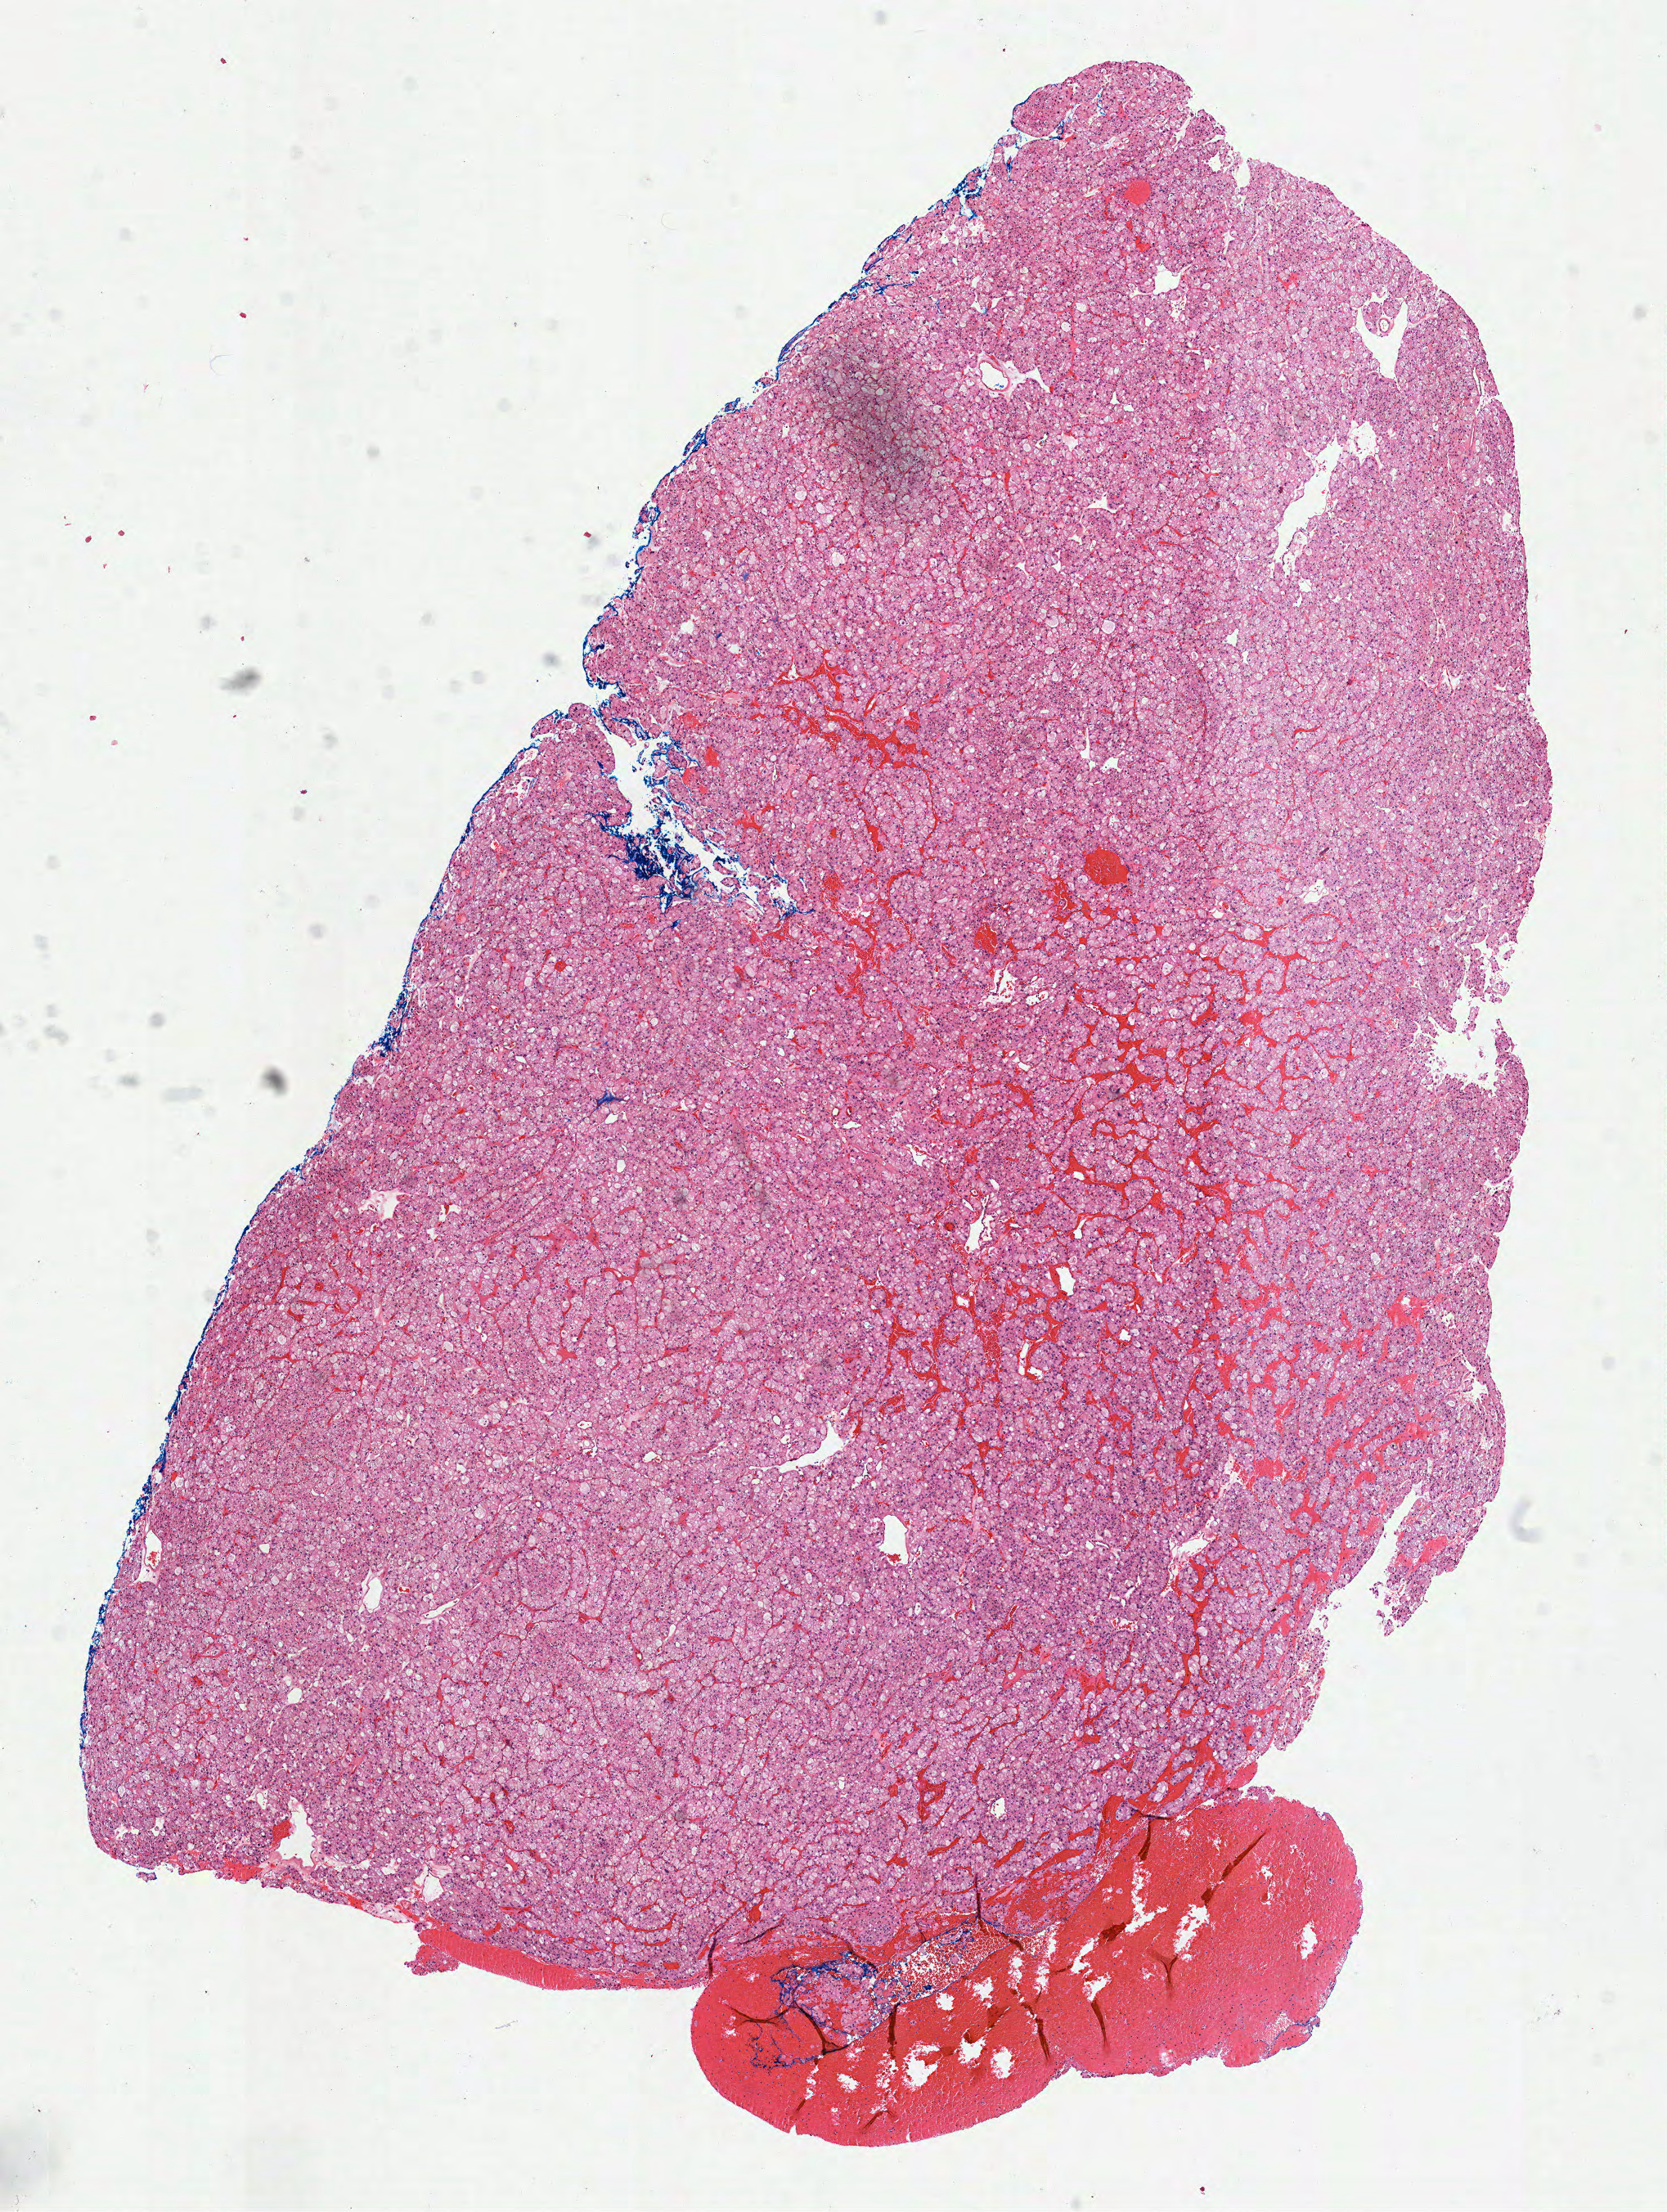
Digitized H&E tissue section (whole slide) — shown as a low-resolution overview of the whole scanned area (about 8.2 x 10.9 mm, acquisition: 40x scan); FFPE section; kidney, primary tumour sample. Female patient; age at initial diagnosis 79 years.
Diagnosis: Renal cell carcinoma, chromophobe type. AJCC pathologic stage: I (7th edition).